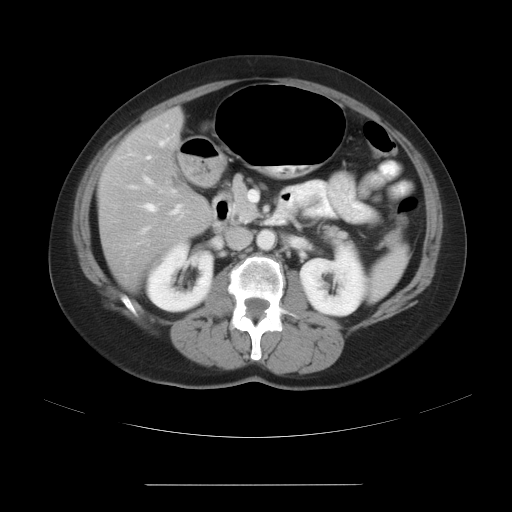
Contrast-enhanced abdominal CT, one axial slice; position 13 of 27 along the scan axis; reconstruction kernel STANDARD; soft-tissue window (W 400 / L 40 HU); 512 × 512 image matrix, field of view 440 × 440 mm. Female patient, age 58 years. Case-level facts recorded for this patient, not image findings: diagnosis: colorectal cancer liver metastases, imaged before liver resection.
Structures marked on this image (manually delineated by an expert):
- hepatic veins: box from (x=135, y=157) to (x=161, y=246) px
- liver: (x=100, y=112)–(x=210, y=285)
- planned liver remnant (the part of the liver to remain after resection): (x=100, y=113)–(x=206, y=210)
- portal vein (with intrahepatic branches): (x=103, y=124)–(x=254, y=241)